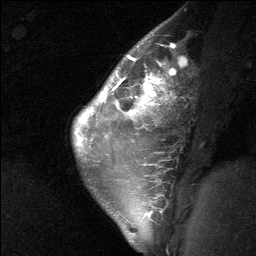
Breast MRI (dynamic contrast-enhanced), one sagittal slice; slice 48 of 64 in the series (ordered by position); dynamic contrast-enhanced study with each time point stored as its own series, time point 2 of 3 at this slice position (early post-contrast, ordered by acquisition time); 1.5 T; TE 4.8 ms, TR 27 ms; 256 × 256 image matrix, field of view 180 × 180 mm. Female patient, age 26 years. From the clinical record (not read from this slice): setting: breast cancer imaged before/during neoadjuvant chemotherapy; receptor status: HR-positive, HER2-negative.
Outlined on this slice (semi-automatic segmentation, software-assisted and operator-edited):
- analysis volume of interest (the breast-tissue region the enhancement analysis was run in; not a lesion): bounding box (x1, y1, x2, y2) in pixels: (86, 43, 179, 138)
- tumour enhancement mask (voxels above the 90 % enhancement threshold inside the analysis volume of interest): (104, 56, 173, 103)